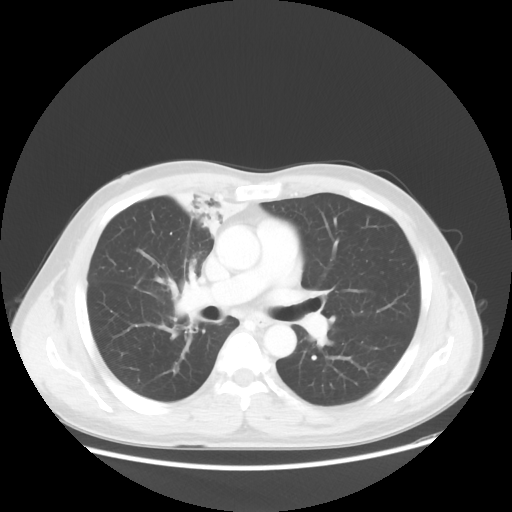
Chest CT, one axial slice; slice 31 of 56 in the series (ordered by position); reconstruction kernel STANDARD; 100 kVp; lung window (W 1500 / L -600 HU); 512 × 512 image matrix. Male patient, age 60 years. From the clinical record (not read from this slice): clinical TNM (as recorded): T2a N1 M0.
Annotated regions visible in this slice (bounding box drawn by a radiologist):
- lung tumour (recorded histology: squamous cell carcinoma): bounding box <165,177,252,245> (left, top, right, bottom; pixels)